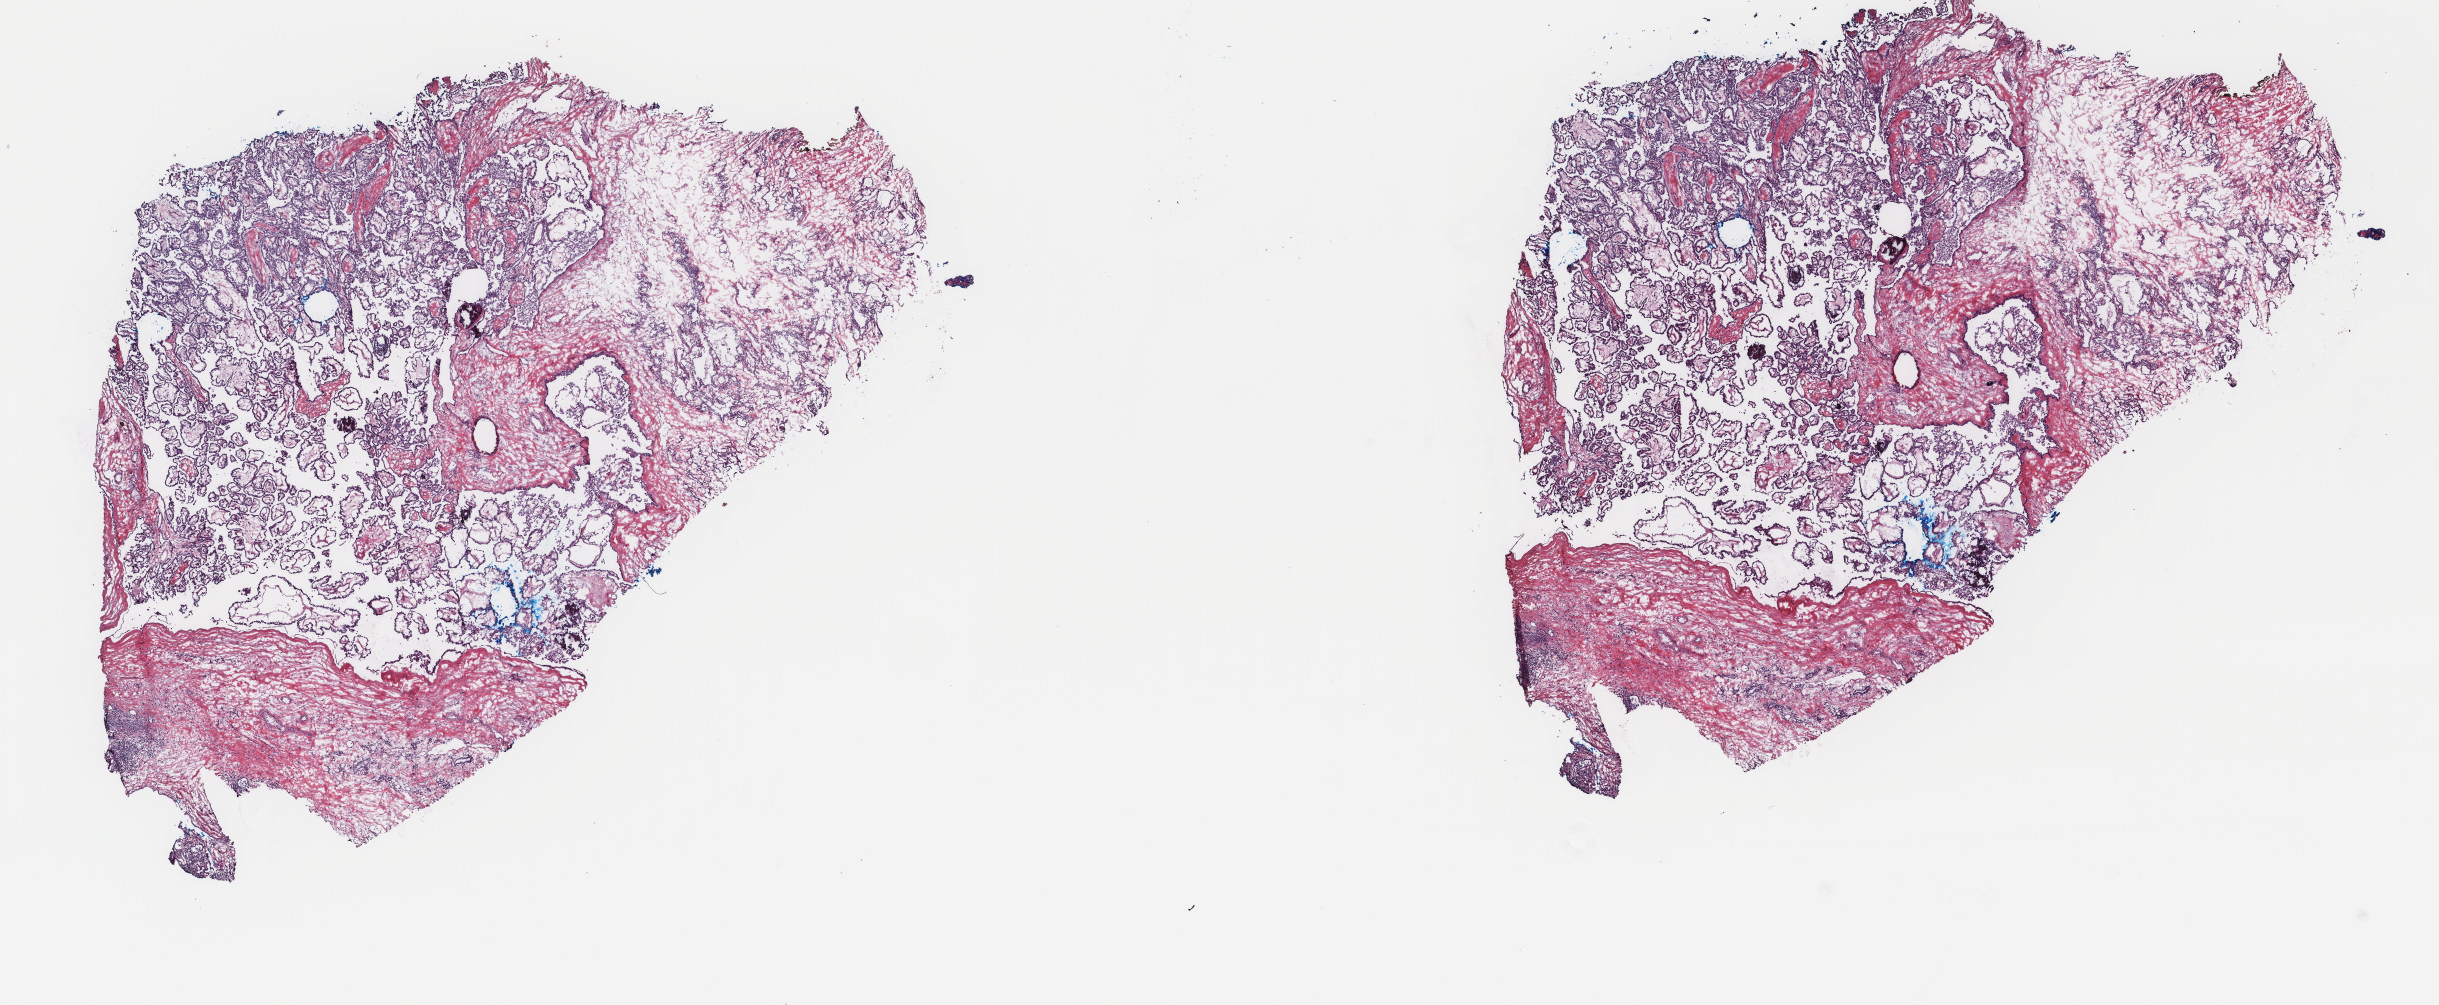
Digitized Hematoxylin and eosin (H&E) stained tissue section (whole slide), a low-resolution overview of the entire scanned area, about 19.4 x 8.0 mm (from a 40x scan), frozen section from the top of the tissue portion, sample: primary tumour, thyroid. Female patient; age at initial diagnosis 34 years. Pathologist review of this section (percent, as recorded): tumour cells 50%, tumour nuclei 90%, normal cells 5%, stromal cells 45%, necrosis 0%. Inflammatory infiltration, as recorded: lymphocyte infiltration 4%, monocyte infiltration 1%, neutrophil infiltration 0%.
Pathologic diagnosis: Papillary adenocarcinoma, NOS (thyroid gland). AJCC pathologic stage: I (7th edition). Lymph nodes positive (case pathology): 0 of 1 examined.